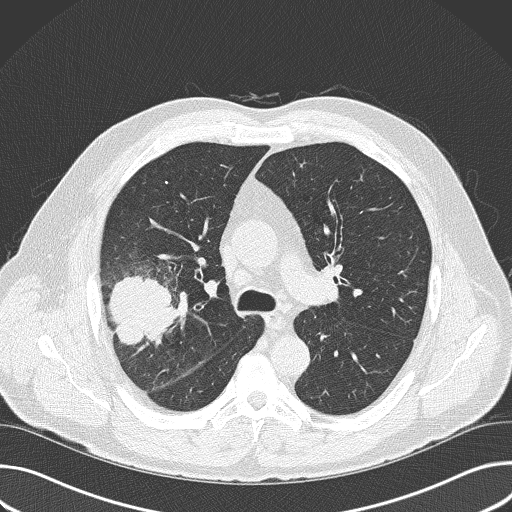
Axial slice from a low-dose chest CT screening exam. First (baseline) screen. Lung window (W 1500 / L -600 HU). 2 mm slice thickness. Slice 106 of 157 in the series. 512 × 512 image matrix, field of view 380 × 380 mm. Male participant, aged 56 years at enrolment. Current smoker at enrolment.
Lesion marked by an expert reader, box from (x=82, y=264) to (x=187, y=372) px. Reader record for this screening exam (exam-level; its link to the box is not recorded): non-calcified nodule or mass ≥4 mm, right upper lobe, 6 × 5 mm, spiculated (stellate) margins, soft tissue attenuation. Participant outcome: lung cancer diagnosed 16 days after this screen — adenocarcinoma, NOS, right upper lobe, poorly differentiated (G3), stage IIB (AJCC 6th edition), 60 mm at pathology.